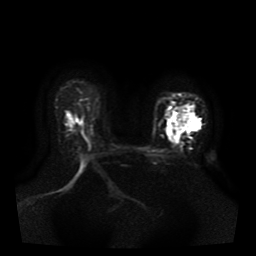
Breast MRI, one axial slice. Position 28 of 41 along the scan axis. Diffusion-weighted series; image 2 of 4 stored at this slice position (different b-values; order by instance number). 1.5 T. 5 mm slice thickness. 256 × 256 image matrix, field of view 330 × 330 mm. Female patient.
Structures marked on this image (manually delineated by an expert):
- tumour on diffusion-weighted imaging: box from (x=168, y=107) to (x=198, y=142) px